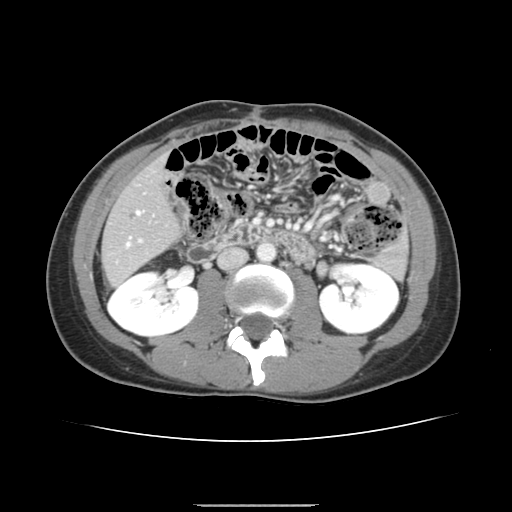
Contrast-enhanced abdominal CT, one axial slice; position 54 of 150 along the scan axis; intravenous contrast given; soft-tissue window (W 400 / L 40 HU); 2.5 mm slice thickness; 512 × 512 image matrix, field of view 324 × 324 mm. Female patient, age 32 years. Case-level facts recorded for this patient, not image findings: diagnosis: colorectal cancer liver metastases, imaged before liver resection; multiple liver metastases: yes; largest metastasis: 0.7 cm; disease in both lobes: no.
Annotated regions visible in this slice (expert manual segmentation):
- hepatic veins: bounding box <126,211,140,247> (left, top, right, bottom; pixels)
- liver: <103,160,179,285>
- planned liver remnant (the part of the liver to remain after resection): <103,160,178,285>
- portal vein (with intrahepatic branches): <130,238,142,241>